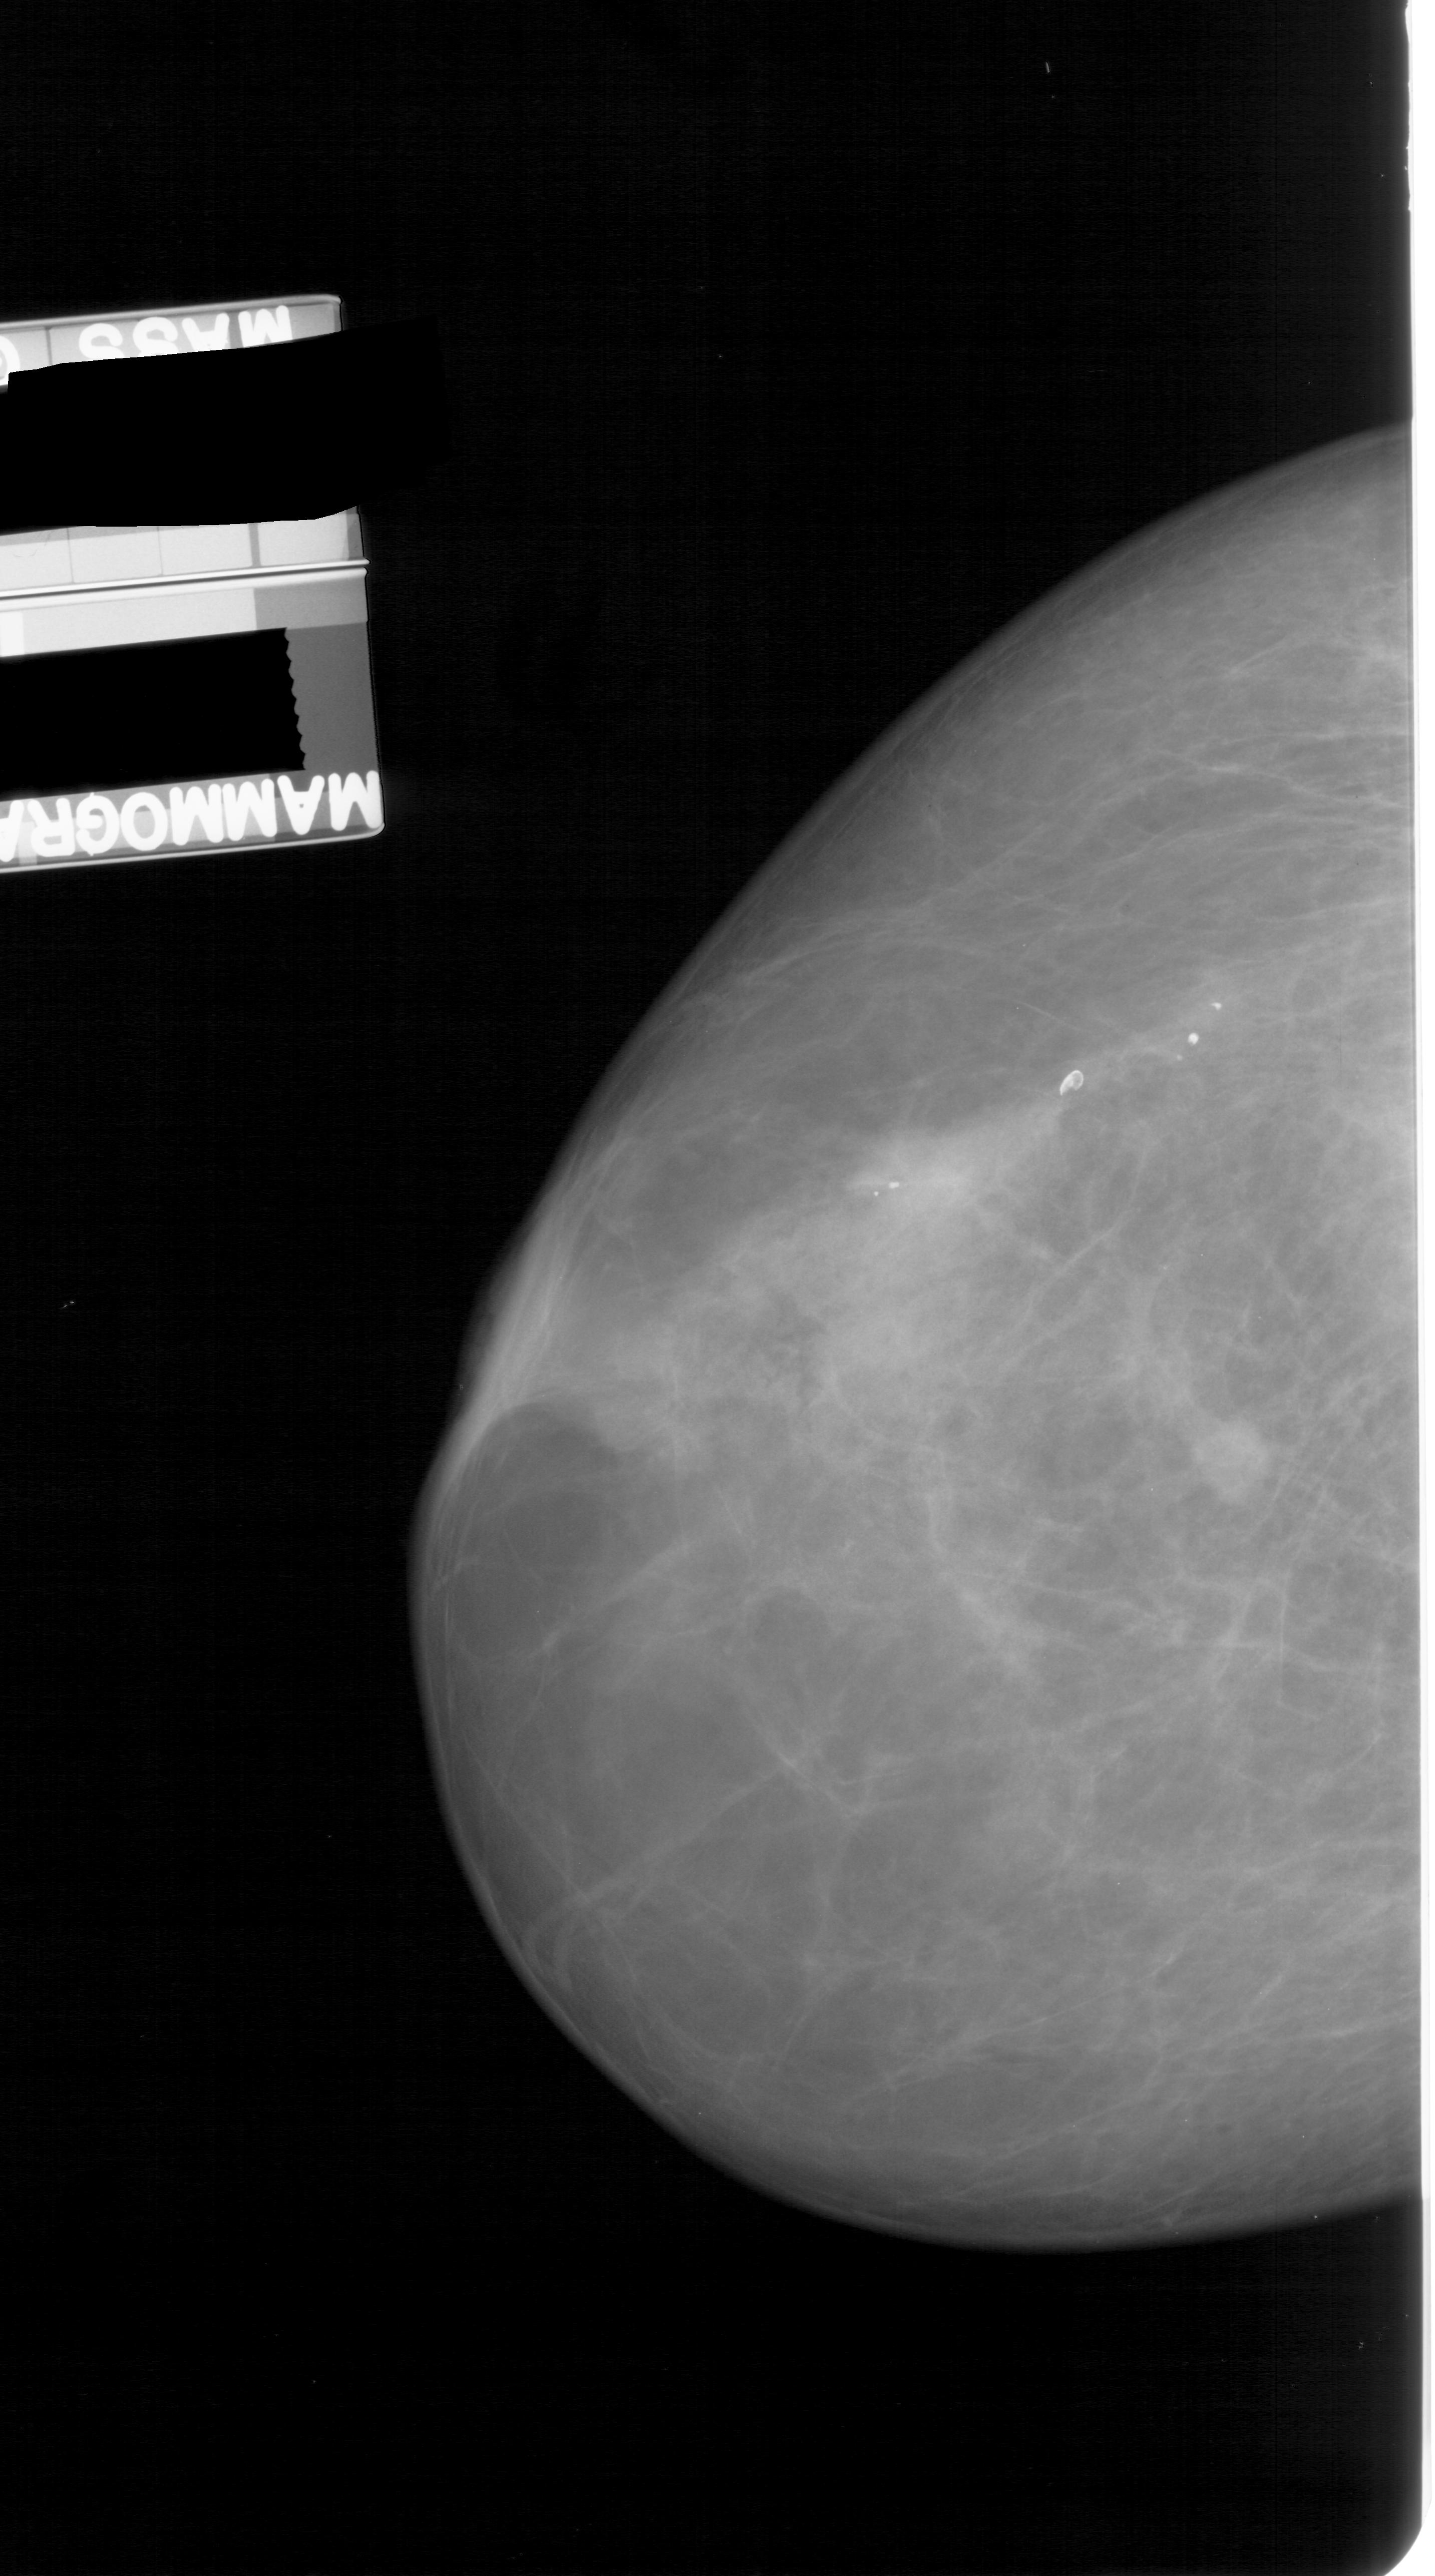
Digitized screen-film mammogram; left breast; CC view; BI-RADS breast density category 4 (scale 1–4); 1435 × 2576 image matrix.
Expert-marked regions of interest on this image (one box per marked abnormality):
- mass, shape oval, margins spiculated; BI-RADS assessment category 4; subtlety rating 3 on a 1 (subtle) to 5 (obvious) scale; pathology result (as recorded, not read from the image): malignant: bounding box <1186,1405,1286,1508> (left, top, right, bottom; pixels)